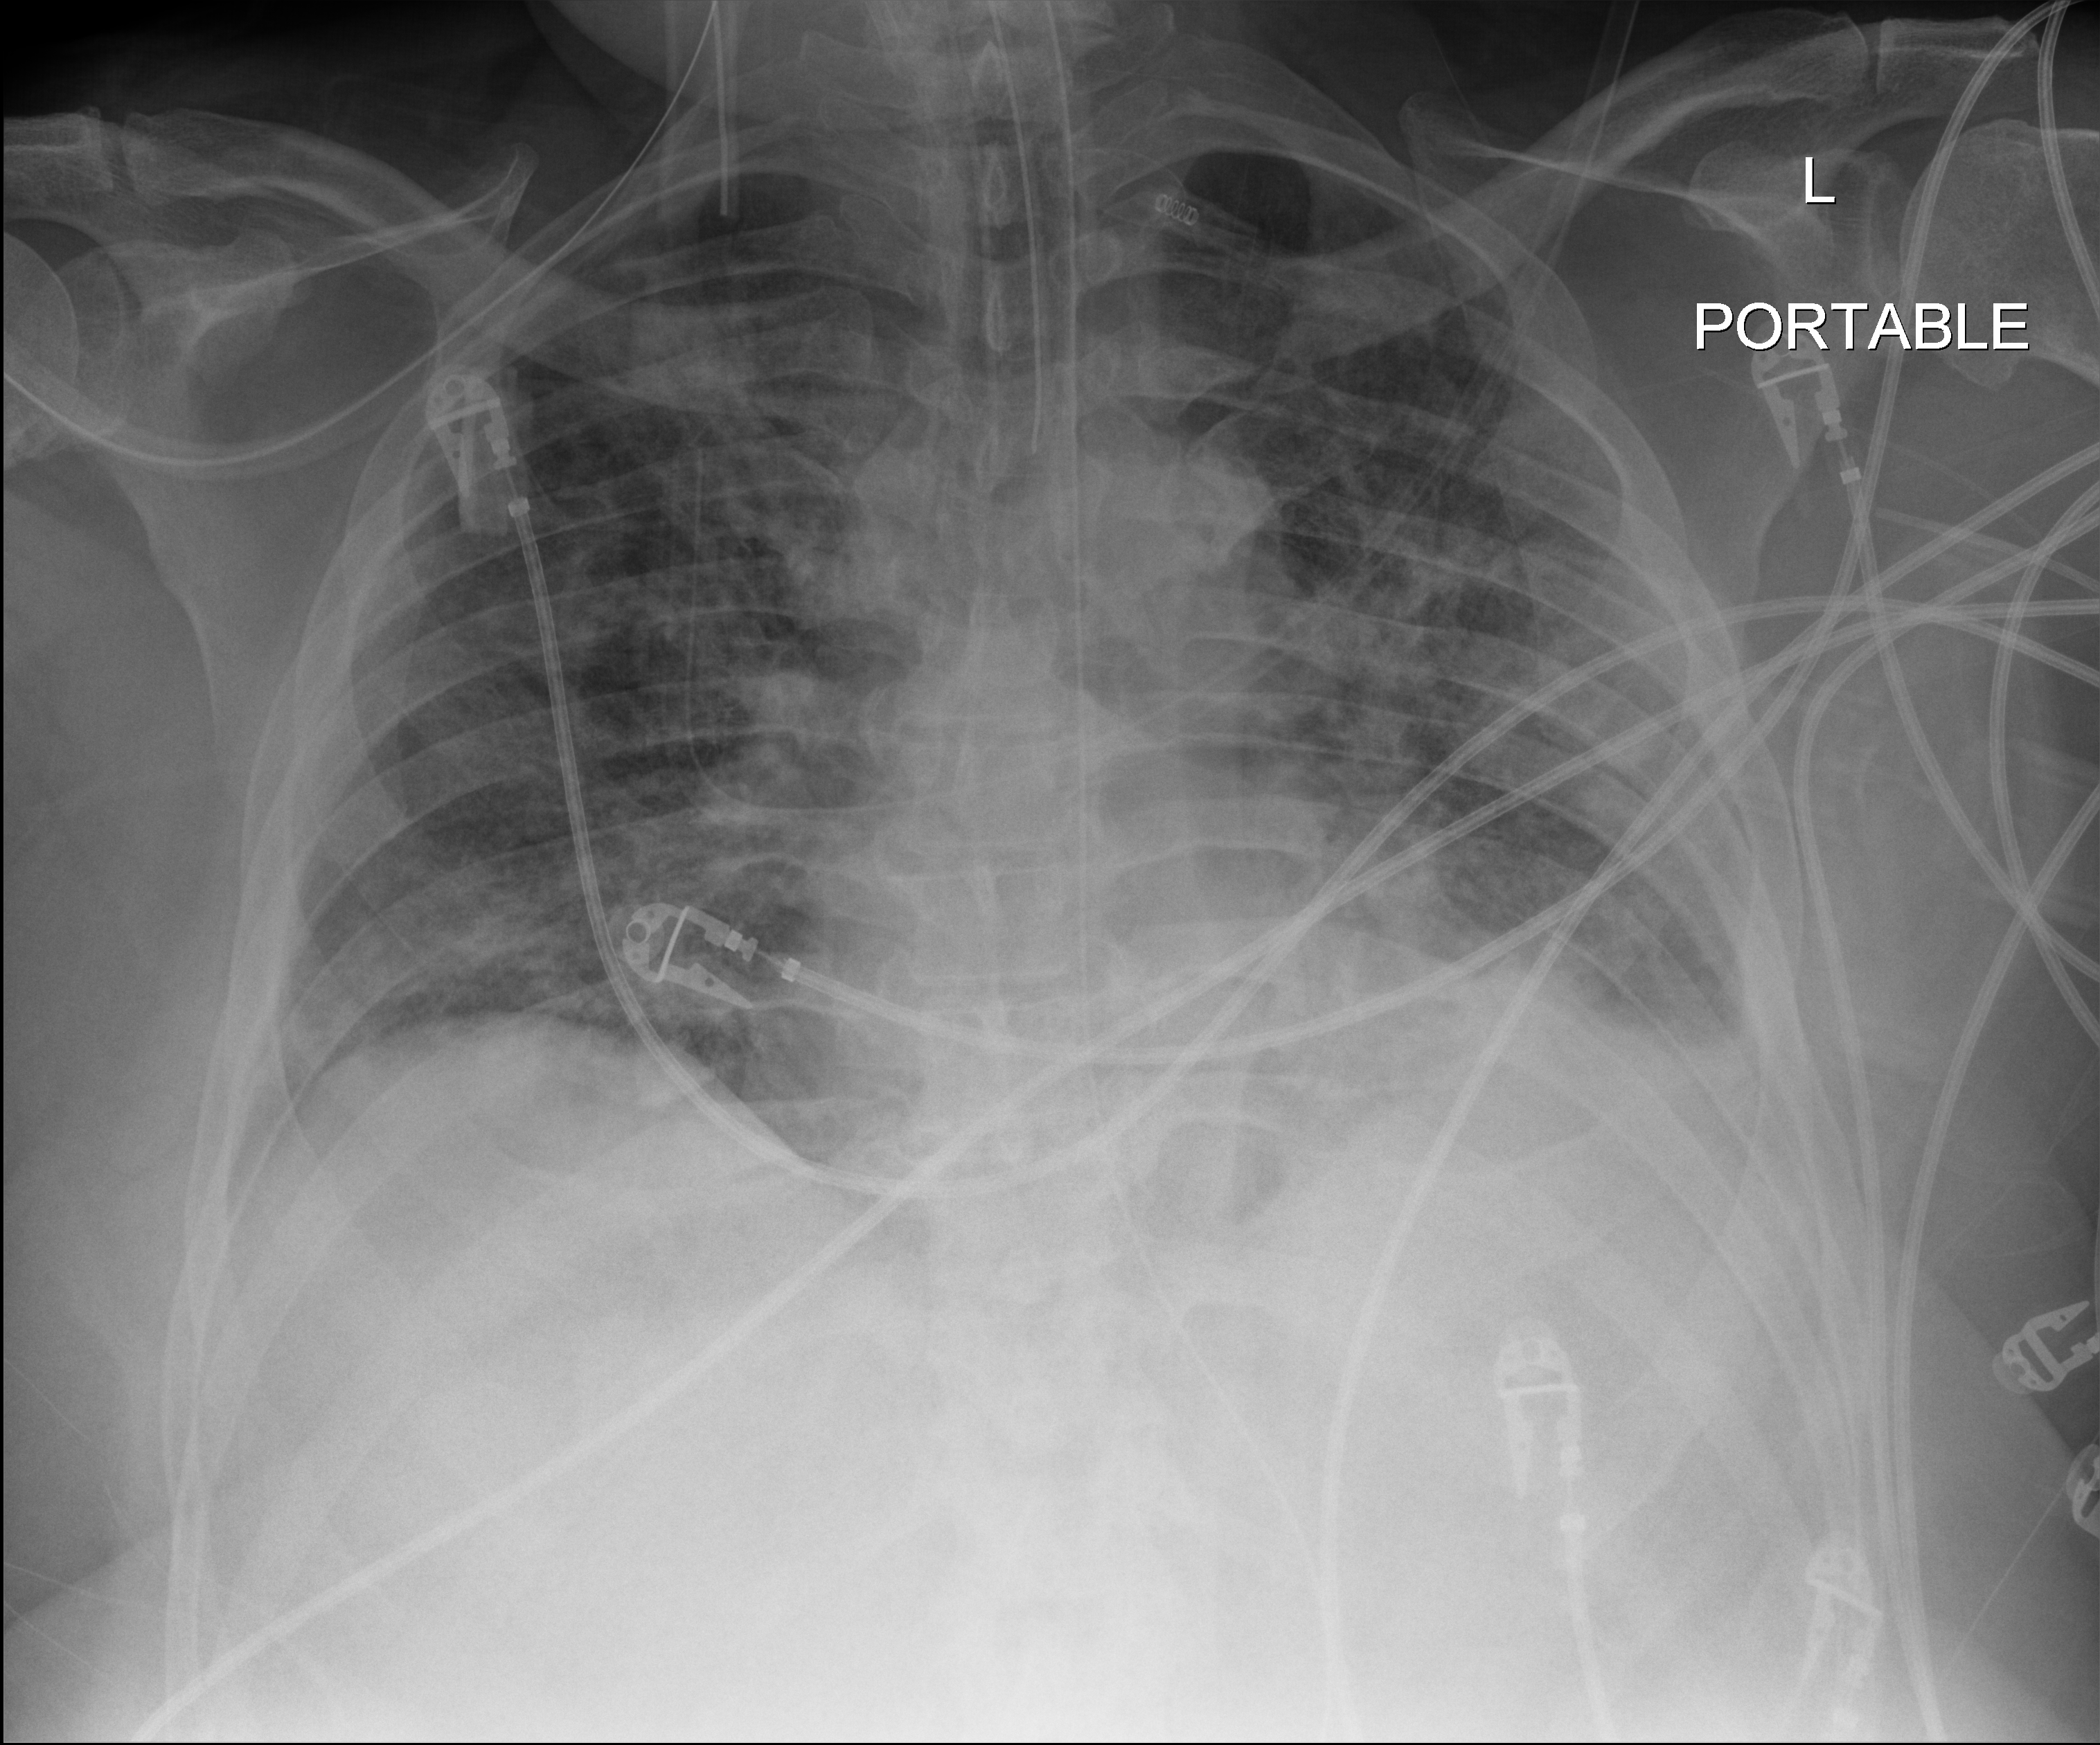
Chest X-ray (portable). Patient hospitalised with COVID-19; male, aged 18–59 years.
Admission-level facts for this patient (not findings on this image; timing relative to this image not recorded): COPD (admission record): no.